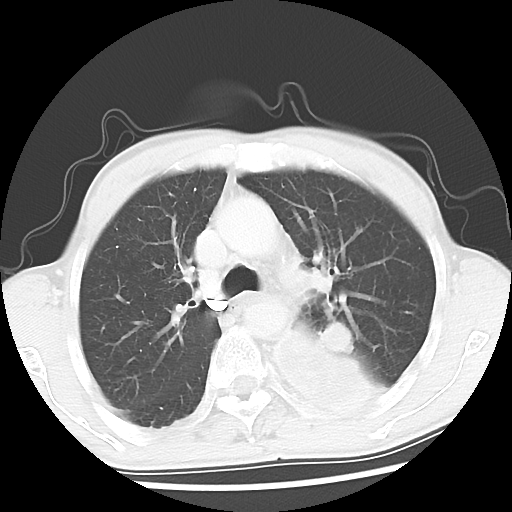
Chest CT, one axial slice. Slice 35 of 52 in the series (ordered by position). Reconstruction kernel LUNG. Lung window (W 1500 / L -600 HU). 512 × 512 image matrix. Patient: male, 60 years. Case-level facts recorded for this patient, not image findings: clinical TNM (as recorded): T4 N0 M0.
Annotated regions visible in this slice (bounding box drawn by a radiologist):
- lung tumour (recorded histology: squamous cell carcinoma): bounding box <264,307,385,423> (left, top, right, bottom; pixels)